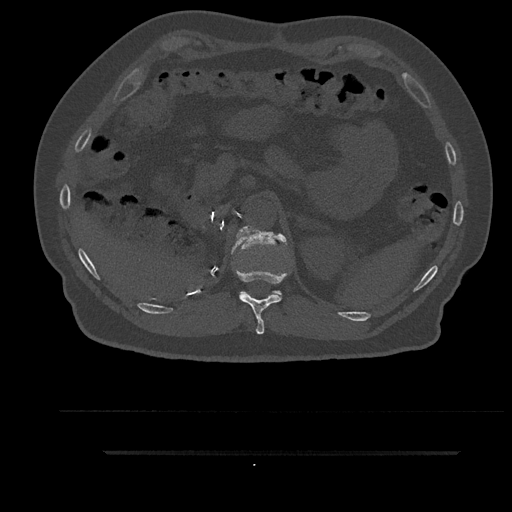
CT including the spine, one axial slice; position 281 of 797 along the scan axis; reconstruction kernel Br40s/3; 120 kVp; bone window (W 1800 / L 400 HU); 0.5 mm slice thickness; 512 × 512 image matrix, field of view 432 × 432 mm. Male patient, age 63 years. Case-level facts recorded for this patient, not image findings: primary cancer: renal.
Annotated regions visible in this slice (semi-automatically segmented with operator editing):
- T11 vertebra: bounding box (x1, y1, x2, y2) in pixels: (236, 232, 289, 335)
- T12 vertebra: (231, 226, 287, 296)